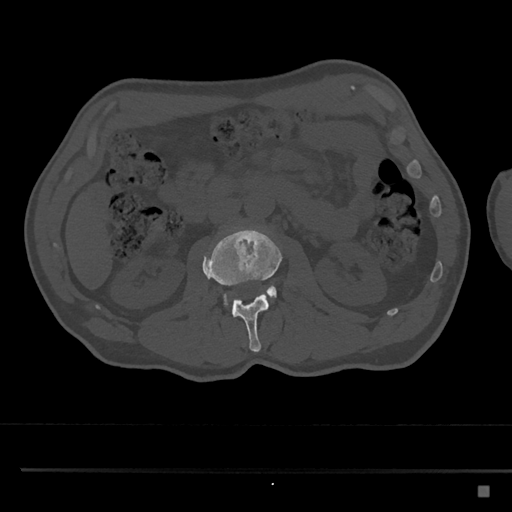
CT including the spine, one axial slice. Slice 743 of 797 in the series (ordered by position). Bone window (W 1800 / L 400 HU). 0.5 mm slice thickness. 512 × 512 image matrix, field of view 391 × 391 mm. Male patient, age 59 years. From the clinical record (not read from this slice): primary cancer: prostate.
Annotated regions visible in this slice (semi-automatic segmentation, software-assisted and operator-edited):
- L2 vertebra: bounding box (x1, y1, x2, y2) in pixels: (202, 227, 282, 353)
- L3 vertebra: (223, 286, 277, 307)